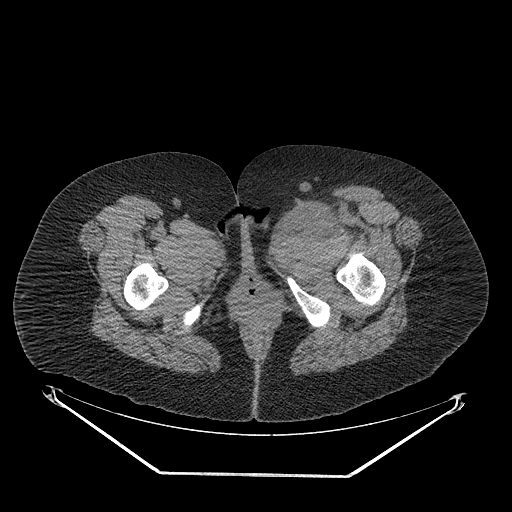
CT of an extremity soft-tissue mass (from a PET/CT study), one axial slice; slice 43 of 267 in the series (ordered by position); reconstruction kernel STANDARD; 140 kVp; soft-tissue window (W 400 / L 40 HU); 512 × 512 image matrix. Female patient. Case-level facts recorded for this patient, not image findings: histological type: myxofibrosarcoma; grade: intermediate; site of the primary tumour: left thigh.
Annotated regions visible in this slice (expert contour drawn on MRI and transferred to this co-registered scan by the dataset authors):
- gross tumour volume including surrounding oedema: bounding box [x1, y1, x2, y2] px = [265, 203, 362, 254]
- gross tumour volume (mass): [283, 203, 336, 238]